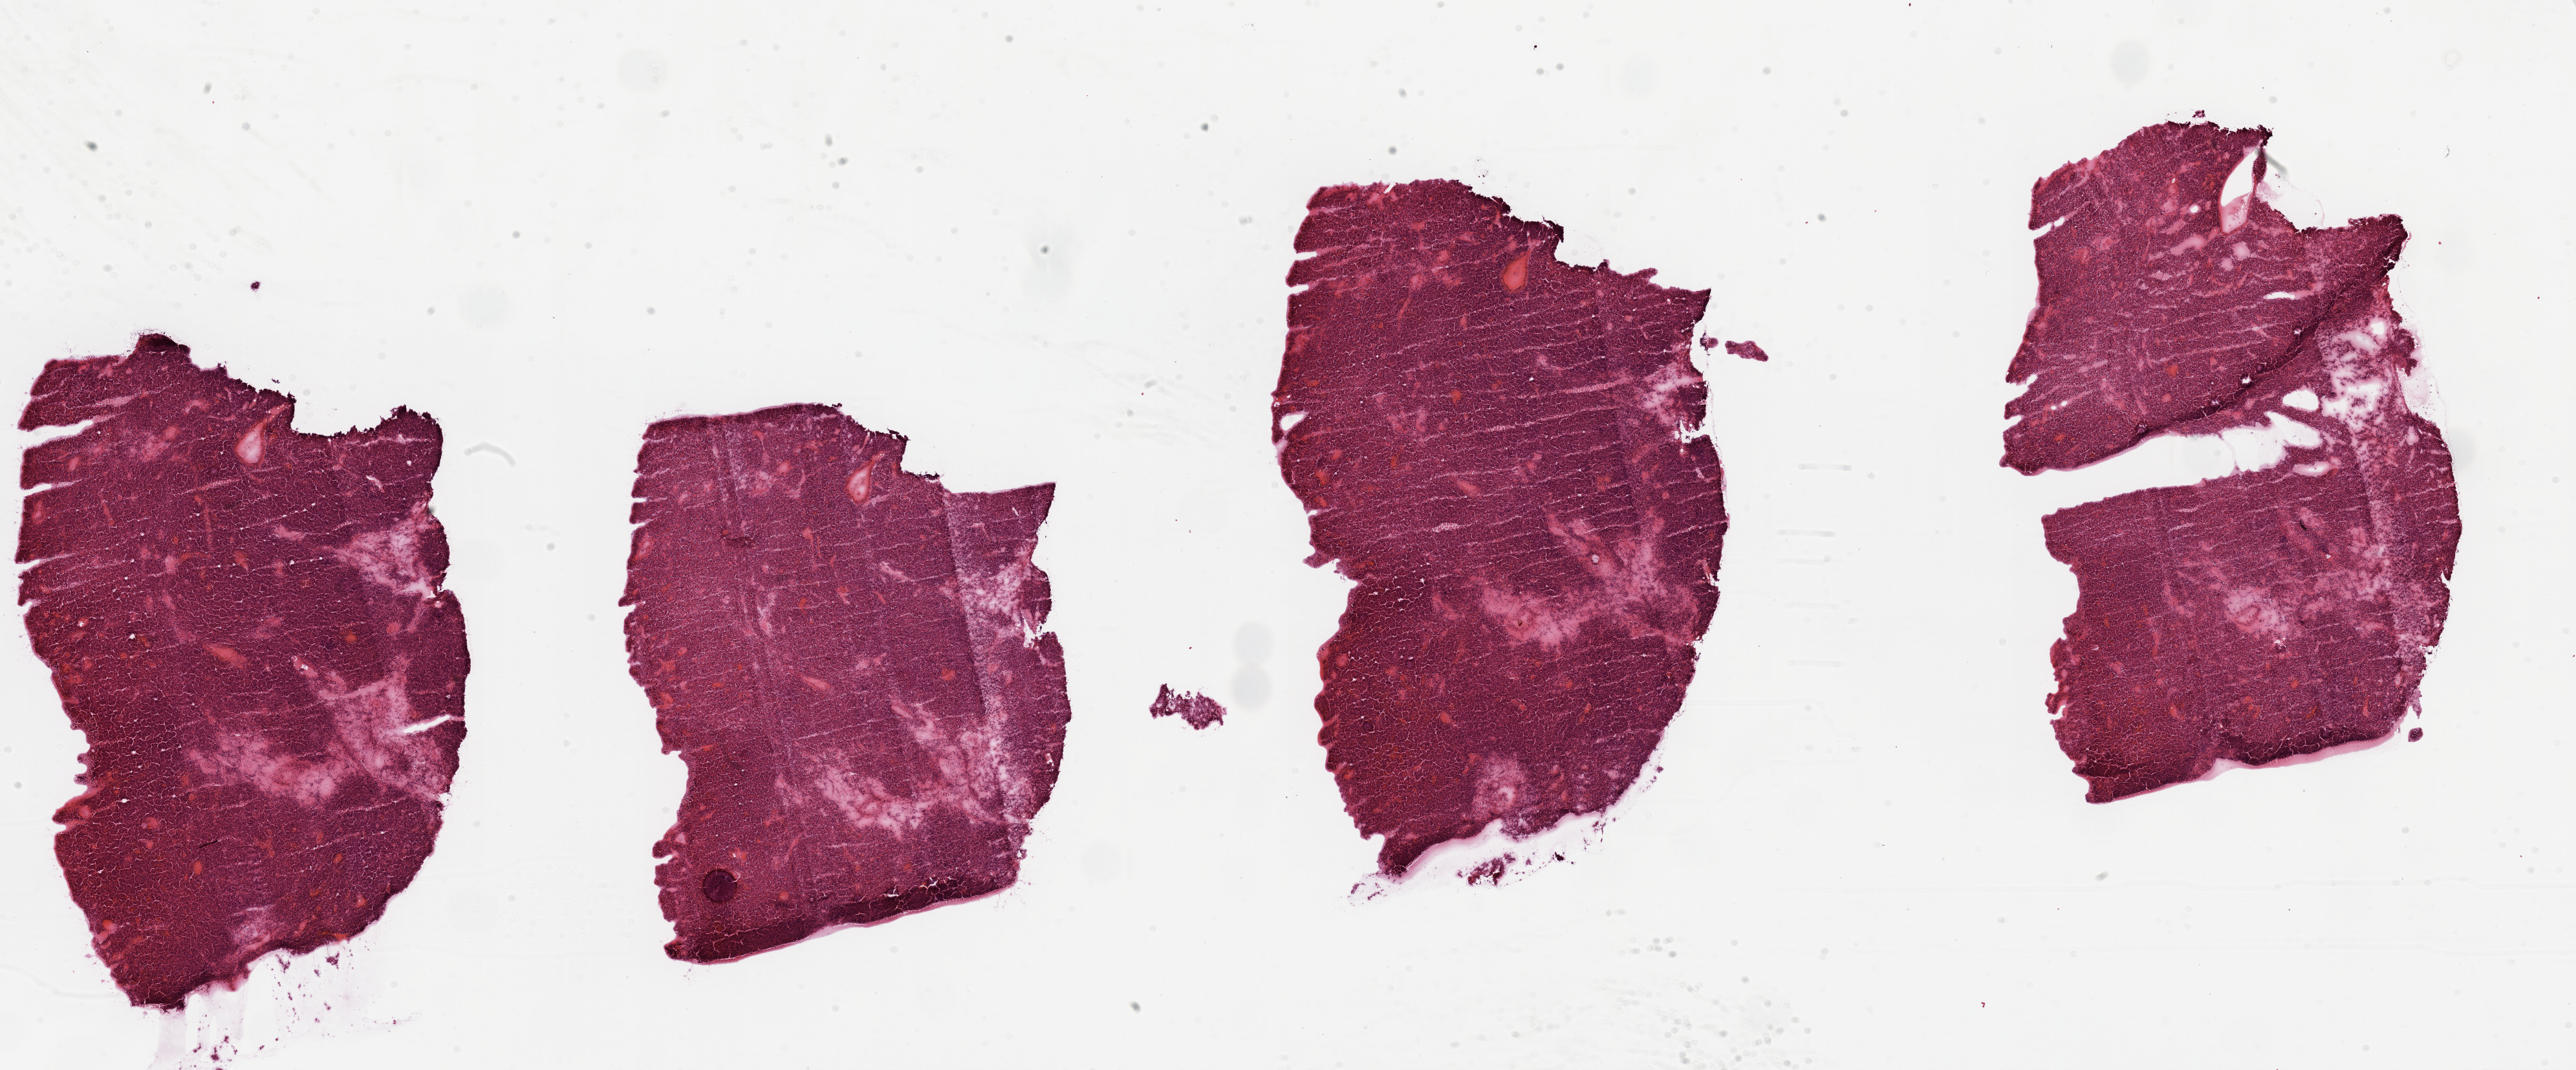
Whole-slide histology image, Hematoxylin and eosin (H&E) stained — a low-resolution overview of the entire scanned area, about 31.5 x 13.1 mm (acquisition: 20x scan); tumour tissue sample, sampled site: kidney. Male, 67 y/o. Histologic grade: G2 (moderately differentiated). Pathologist review of this section (percent, as recorded): tumour nuclei 90%, necrosis 5%.
AJCC pathologic stage: III. Diagnosis: Renal cell carcinoma, NOS. Primary tumour site (as recorded): middle.